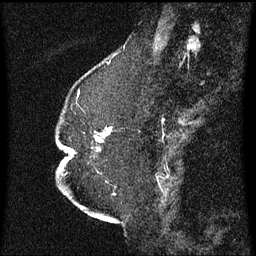
Breast MRI (dynamic contrast-enhanced), one sagittal slice. Slice 21 of 60 in the series (ordered by position). Dynamic contrast-enhanced series, image 2 of 3 at this slice position (ordered by acquisition). 1.5 T. TE 4.2 ms, TR 8.4 ms. 2.3 mm slice thickness. 256 × 256 image matrix, field of view 200 × 200 mm. Patient: female, 52 years. Case-level facts recorded for this patient, not image findings: setting: breast cancer imaged before/during neoadjuvant chemotherapy; receptor status: HR-positive, HER2-negative.
Structures marked on this image (semi-automatically segmented with operator editing):
- analysis volume of interest (the breast-tissue region the enhancement analysis was run in; not a lesion): bounding box (x1, y1, x2, y2) in pixels: (65, 128, 113, 175)
- tumour enhancement mask (voxels above the 70 % enhancement threshold inside the analysis volume of interest): (96, 128, 112, 143)